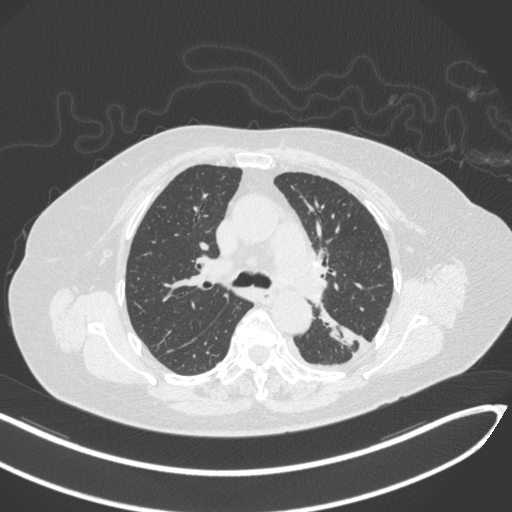
Chest CT, one axial slice; slice 205 of 270 in the series (ordered by position); reconstruction kernel B31f; 120 kVp; lung window (W 1500 / L -600 HU); 1 mm slice thickness; 512 × 512 image matrix. Patient: female, 76 years. From the clinical record (not read from this slice): clinical TNM (as recorded): T1c N0 M0.
Outlined on this slice (rectangle marked by the reading radiologist):
- lung tumour (recorded histology: adenocarcinoma): bounding box <315,303,360,348> (left, top, right, bottom; pixels)